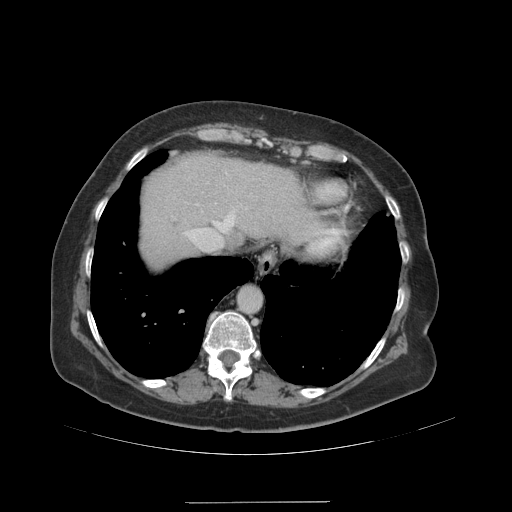
Contrast-enhanced abdominal CT (liver protocol), one axial slice. Slice 83 of 99 in the series (ordered by position). Reconstruction kernel STANDARD. 140 kVp. Soft-tissue window (W 400 / L 40 HU). 2.5 mm slice thickness. 512 × 512 image matrix. From the clinical record (not read from this slice): diagnosis: hepatocellular carcinoma (patient treated with transarterial chemoembolisation; whether this scan precedes or follows treatment is not stated here); TNM stage (as recorded): Stage-IVA; Child-Pugh class: A.
Structures marked on this image (semi-automatic segmentation, software-assisted and operator-edited):
- abdominal aorta: bounding box [x1, y1, x2, y2] px = [238, 286, 261, 312]
- liver parenchyma outside the tumour (the mass and vessels are separate outlines, so this box may not span the whole liver): [141, 152, 318, 268]
- liver vessels: [184, 173, 236, 251]